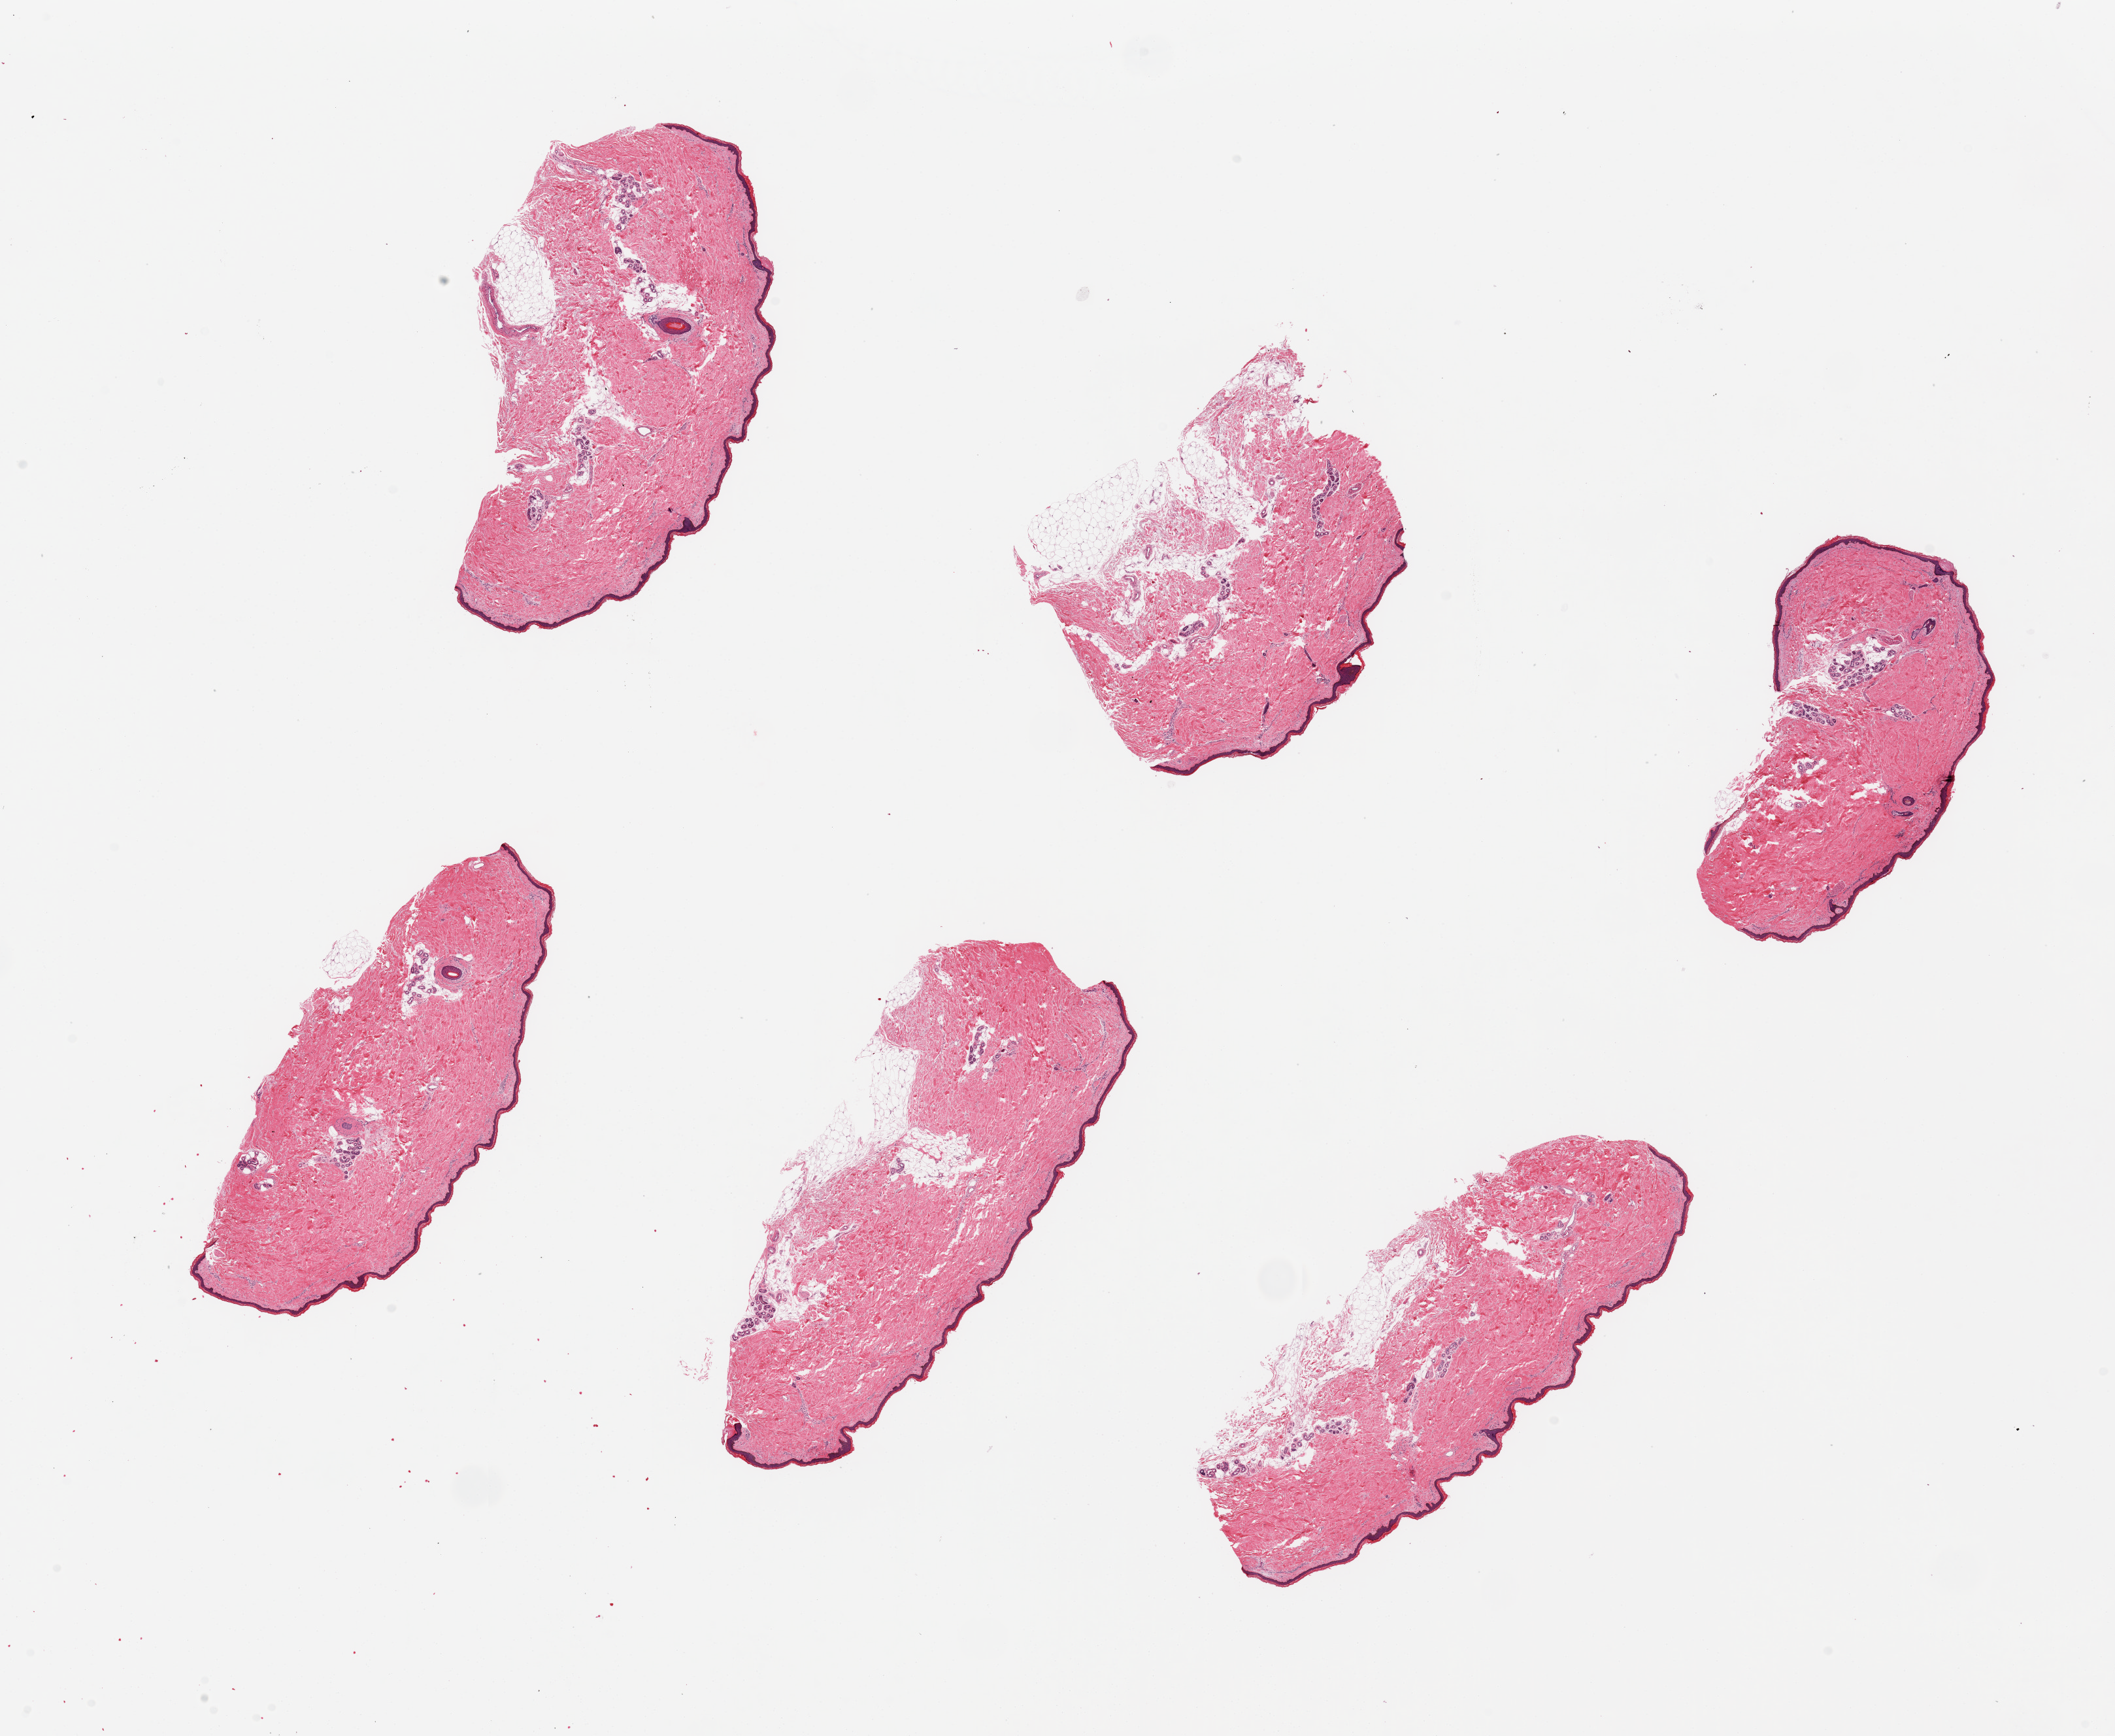
Digitized haematoxylin and eosin-stained section — shown as a low-resolution overview of the whole scanned area (about 25.6 x 21.0 mm), PAXgene-fixed, paraffin-embedded tissue, sampled site (target tissue): skin of lower leg, donor tissue sample.
Review note (as recorded): 6 pieces, ~6x3mm, squamous epithelium is 1-2% thickness.